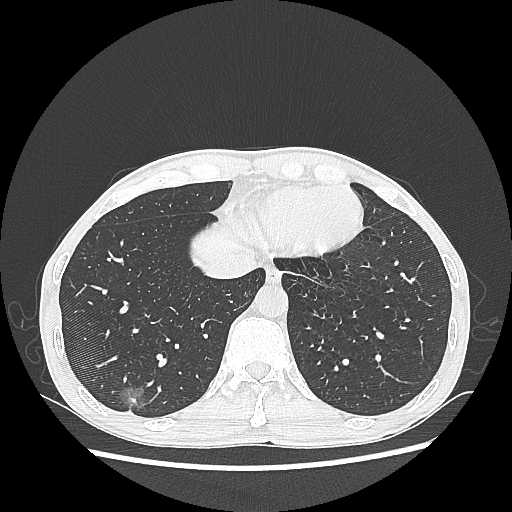
Chest CT, one axial slice. Reconstruction kernel LUNG. 100 kVp. Lung window (W 1500 / L -600 HU). 512 × 512 image matrix, field of view 360 × 360 mm. Male patient, age 60 years. From the clinical record (not read from this slice): clinical TNM (as recorded): T1c N0 M0; histopathological grade: G2.
Outlined on this slice (rectangle marked by the reading radiologist):
- lung tumour (recorded histology: adenocarcinoma): bounding box <113,380,156,415> (left, top, right, bottom; pixels)